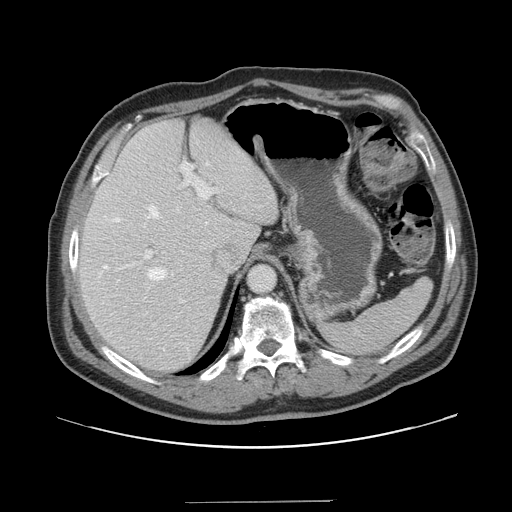
Contrast-enhanced abdominal CT, one axial slice. Slice 111 of 151 in the series (ordered by position). Intravenous contrast given. Soft-tissue window (W 400 / L 40 HU). 2.5 mm slice thickness. 512 × 512 image matrix. Male patient, age 63 years. Case-level facts recorded for this patient, not image findings: diagnosis: colorectal cancer liver metastases, imaged before liver resection; multiple liver metastases: no; largest metastasis: 2.1 cm; disease in both lobes: no.
Outlined on this slice (expert manual segmentation):
- hepatic veins: bounding box (x1, y1, x2, y2) in pixels: (103, 163, 209, 280)
- liver: (78, 118, 278, 373)
- planned liver remnant (the part of the liver to remain after resection): (79, 118, 267, 373)
- portal vein (with intrahepatic branches): (144, 162, 219, 303)